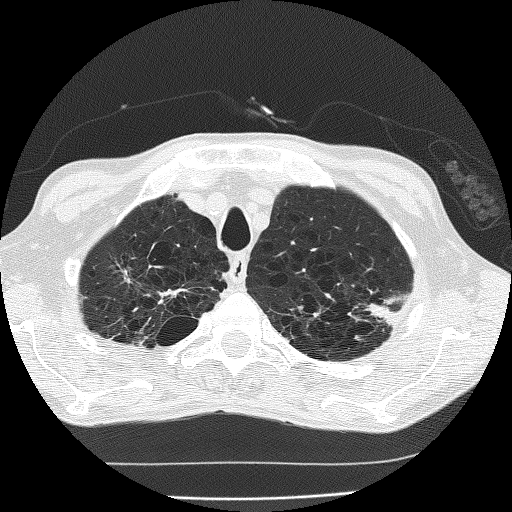
Chest CT (low-dose screening protocol), one axial image, second annual screen, lung window (W 1500 / L -600 HU), 2 mm slice thickness, lung (sharp) reconstruction kernel (FC51). Male, age 60 years at enrolment. Current smoker at enrolment.
Expert-annotated lung lesion, bounding box (x1, y1, x2, y2) in pixels: (346, 281, 414, 343). The screening reader recorded 2 non-calcified nodules or masses ≥4 mm on this exam; which of them this box marks is not recorded. Official screen result: positive, other. Later outcome: lung cancer diagnosed 178 days after this screen — bronchiolo-alveolar carcinoma, mucinous, left upper lobe, stage IV (AJCC 6th edition).